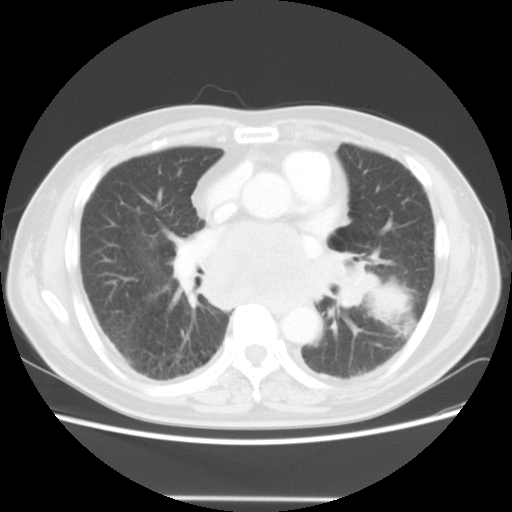
Chest CT, one axial slice; slice 25 of 56 in the series (ordered by position); reconstruction kernel STANDARD; 140 kVp; lung window (W 1500 / L -600 HU); 5 mm slice thickness; 512 × 512 image matrix, field of view 360 × 360 mm. Male patient, age 66 years. From the clinical record (not read from this slice): clinical TNM (as recorded): T4 N3 M0; histopathological grade: G3.
Annotated regions visible in this slice (bounding box drawn by a radiologist):
- lung tumour (recorded histology: small cell carcinoma): bounding box <368,273,410,327> (left, top, right, bottom; pixels)